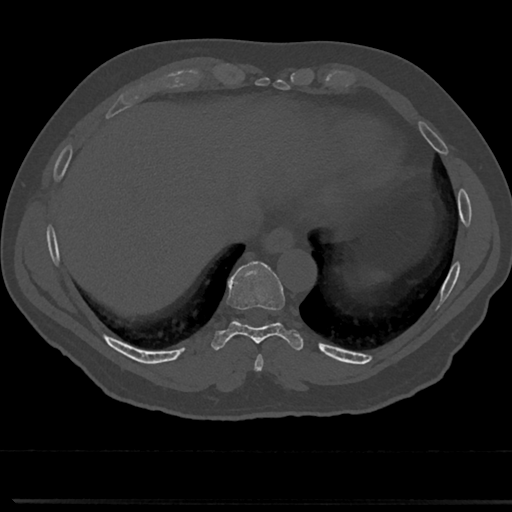
CT including the spine, one axial slice. Position 301 of 817 along the scan axis. Reconstruction kernel Br40s/3. Bone window (W 1800 / L 400 HU). 0.5 mm slice thickness. 512 × 512 image matrix, field of view 355 × 355 mm. Male patient, age 61 years. From the clinical record (not read from this slice): primary cancer: prostate.
Annotated regions visible in this slice (semi-automatic segmentation, software-assisted and operator-edited):
- T8 vertebra: box from (x=235, y=325) to (x=284, y=356) px
- T9 vertebra: (x=232, y=266)–(x=283, y=330)